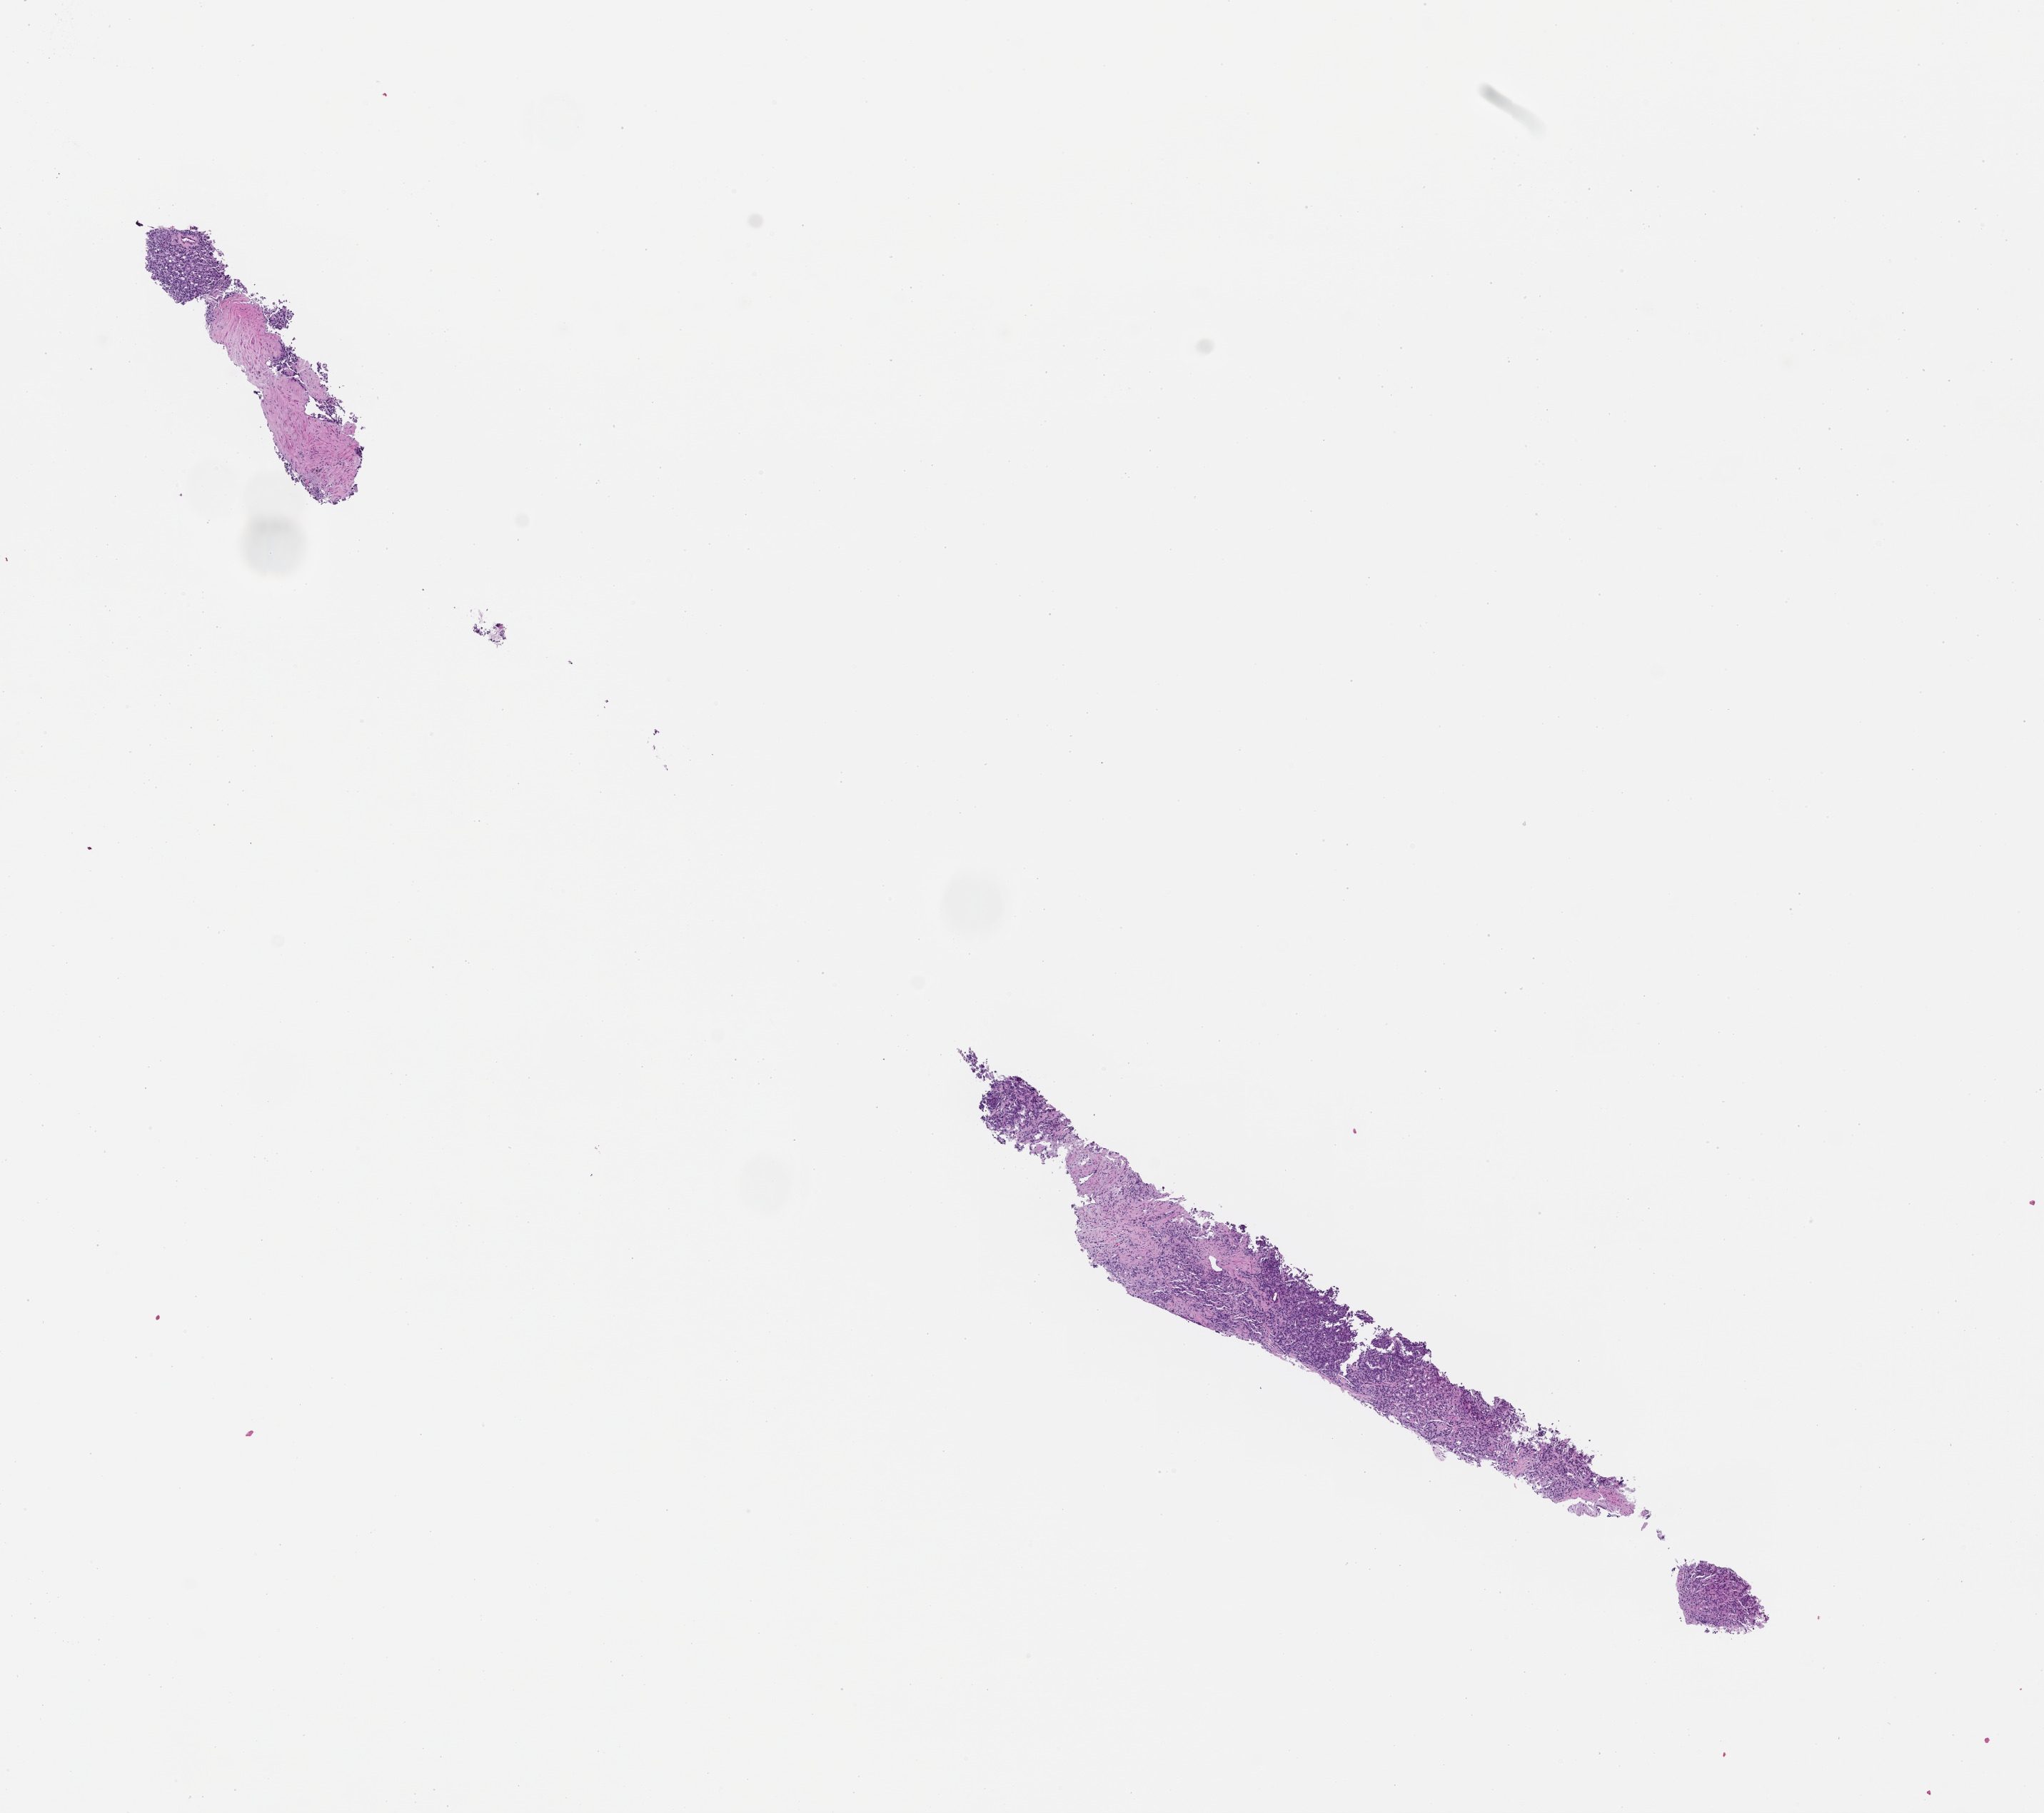
H&E whole-slide image — a low-resolution overview of the entire scanned area, about 11.6 x 10.3 mm. FFPE section. Tissue site: prostate. Archival tissue. Male patient.
This section: primary tumor. Diagnosis: Prostate Carcinoma.